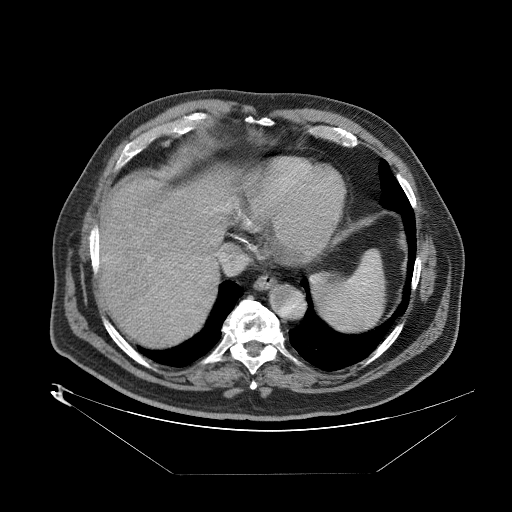
Contrast-enhanced abdominal CT (liver protocol), one axial slice; slice 72 of 89 in the series (ordered by position); reconstruction kernel STANDARD; one of 2 acquisitions stored at this slice position; soft-tissue window (W 400 / L 40 HU); 2.5 mm slice thickness; 512 × 512 image matrix, field of view 480 × 480 mm. From the clinical record (not read from this slice): diagnosis: hepatocellular carcinoma (patient treated with transarterial chemoembolisation; whether this scan precedes or follows treatment is not stated here); TNM stage (as recorded): Stage-II; Child-Pugh class: B; tumour differentiation: moderately differentiated; tumour size: 4 cm.
Structures marked on this image (semi-automatic segmentation, software-assisted and operator-edited):
- abdominal aorta: bounding box [x1, y1, x2, y2] px = [269, 286, 304, 320]
- liver parenchyma outside the tumour (the mass and vessels are separate outlines, so this box may not span the whole liver): [94, 176, 238, 342]
- mass: [151, 252, 216, 315]
- liver vessels: [96, 197, 236, 292]